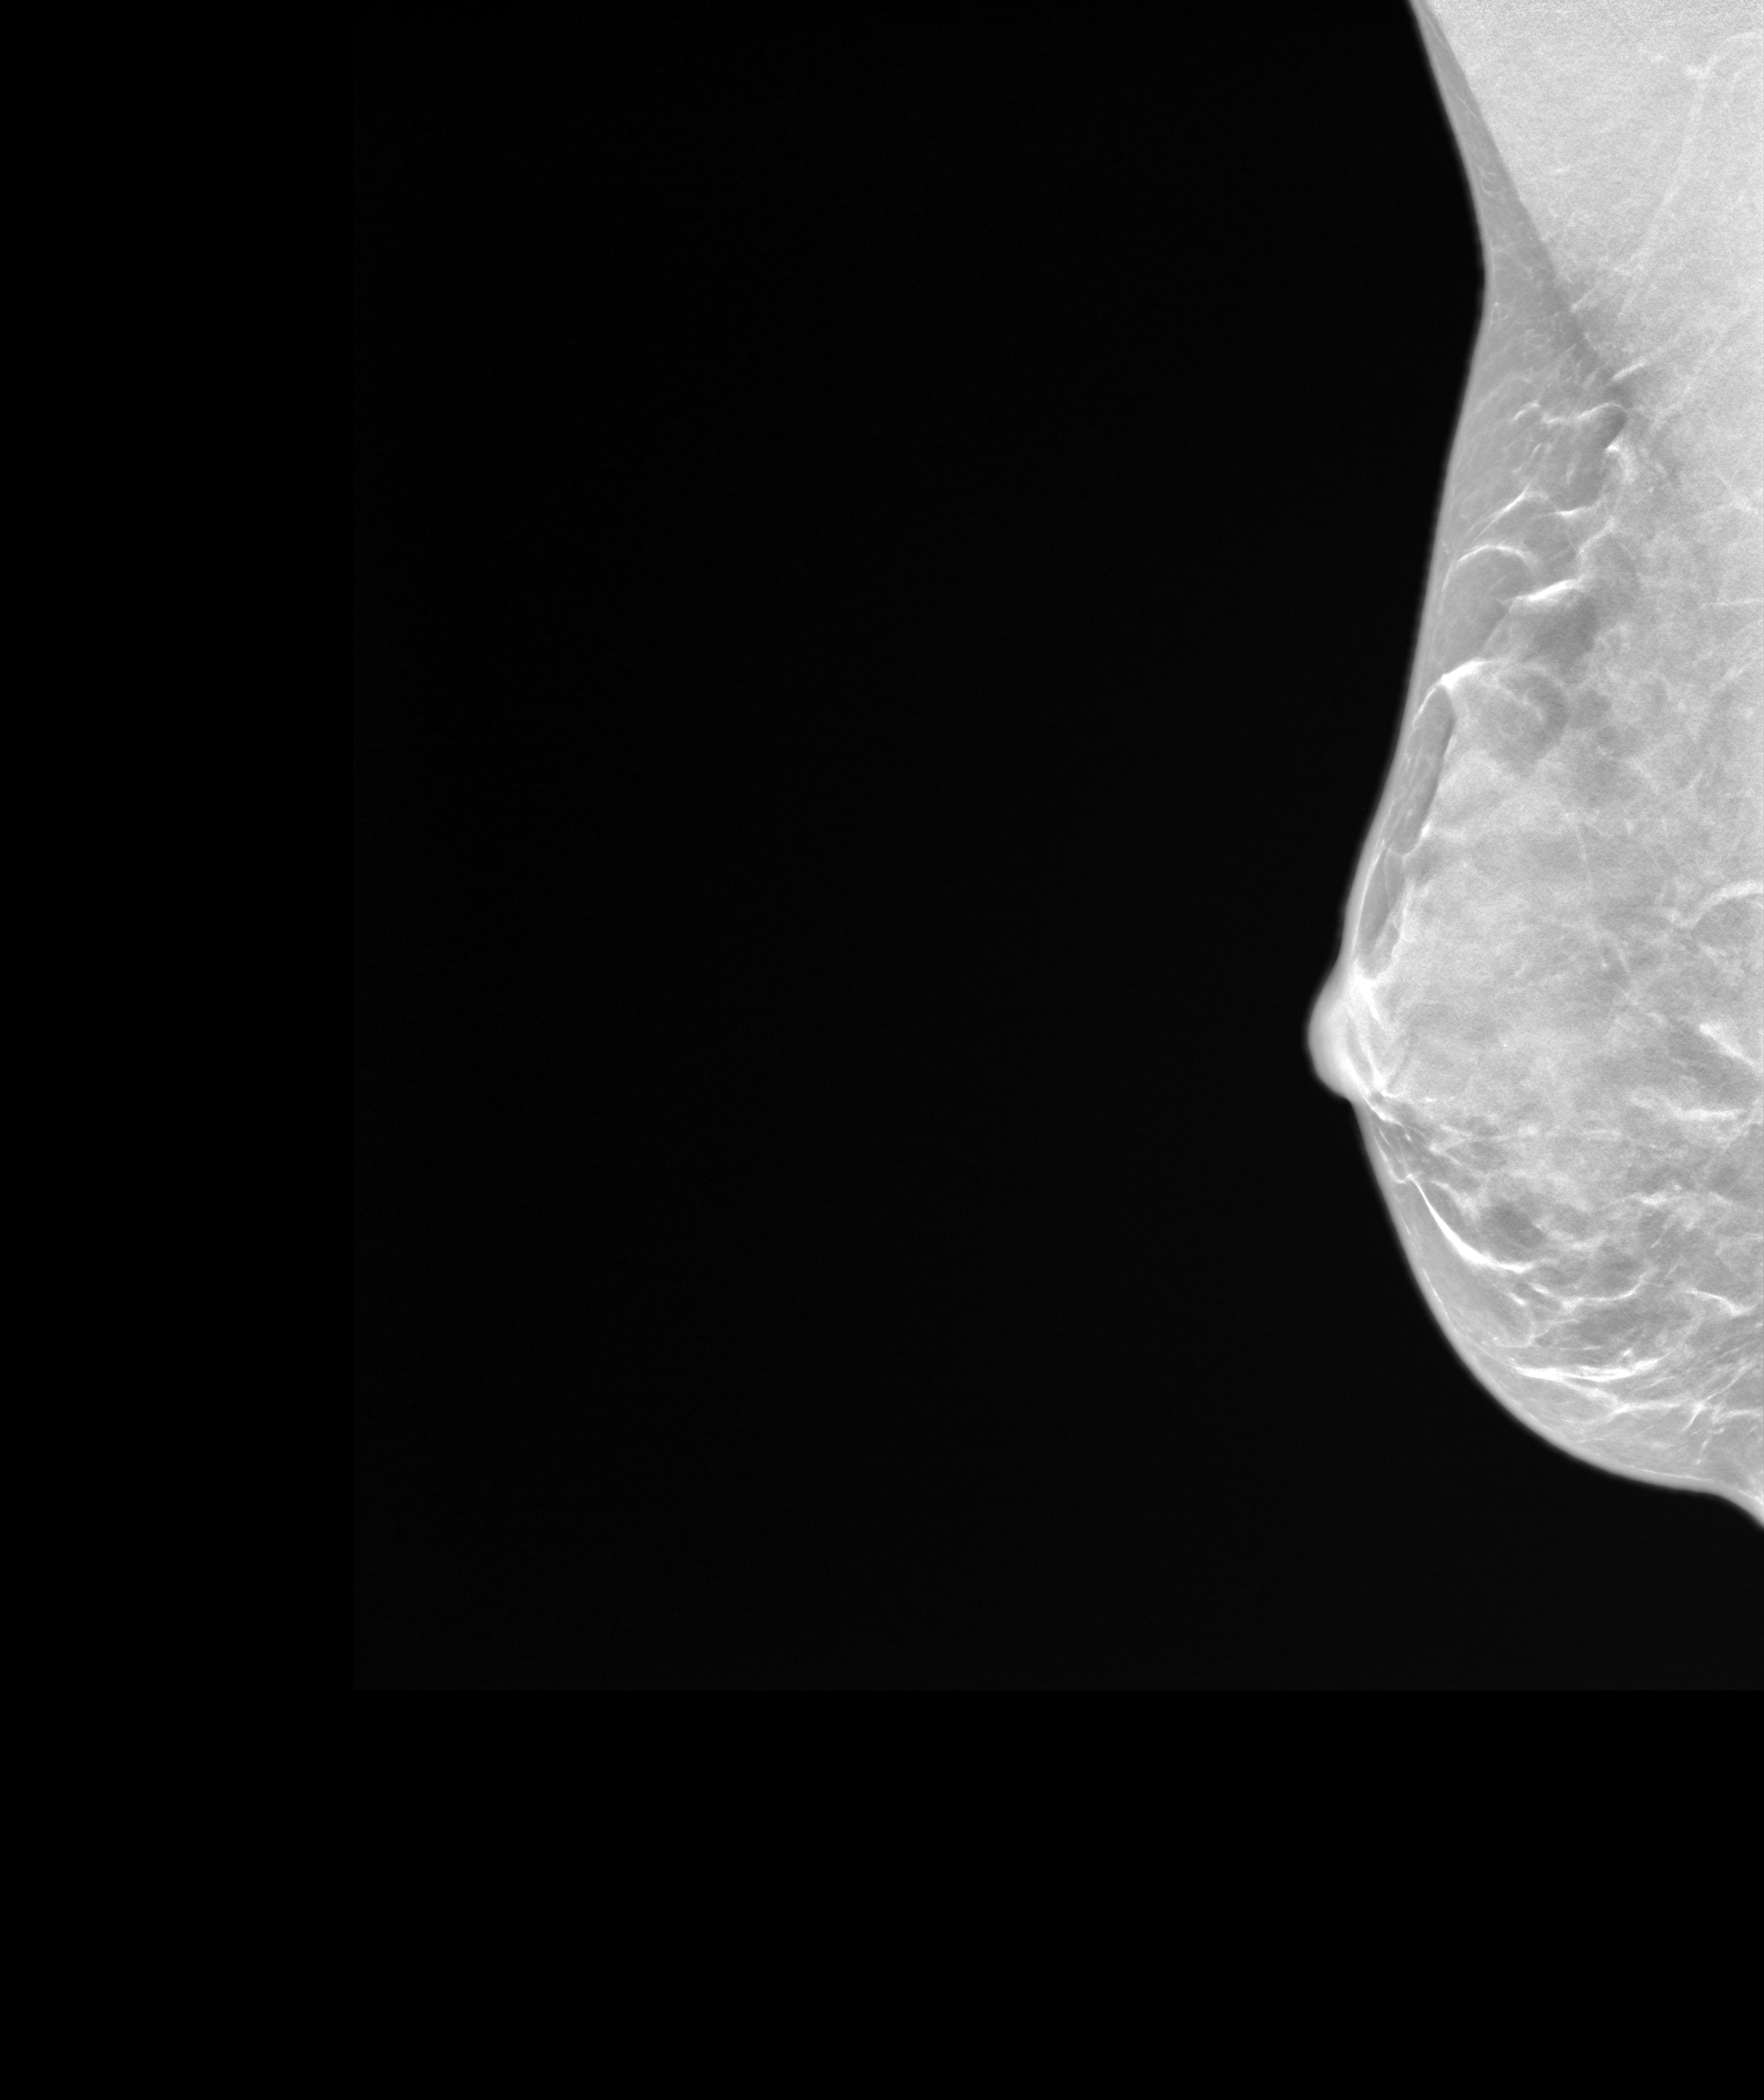
Annual screening mammography examination. Female patient, age 55 years.
Image type: synthesized 2-D view from tomosynthesis. Breast: right. Projection: MLO view.